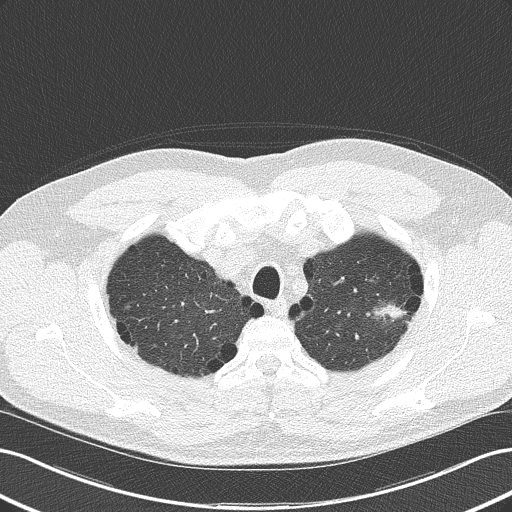
Low-dose screening chest CT, axial slice. Second screening round (one year after baseline). Lung window (W 1500 / L -600 HU). 2 mm slice thickness. Slice 37 of 177 in the series. 512 × 512 image matrix, field of view 360 × 360 mm. Male participant, aged 62 years at enrolment.
Lesion marked by an expert reader, bounding box [x1, y1, x2, y2] px = [356, 286, 419, 340]. The screening reader recorded 2 non-calcified nodules or masses ≥4 mm on this exam (left upper lobe, right middle lobe); which of them this box marks is not recorded. Official screen result: positive, other. Participant outcome: lung cancer diagnosed 46 days after this screen — adenocarcinoma, NOS, left upper lobe, well differentiated (G1), stage IB (AJCC 6th edition), 17 mm at pathology.